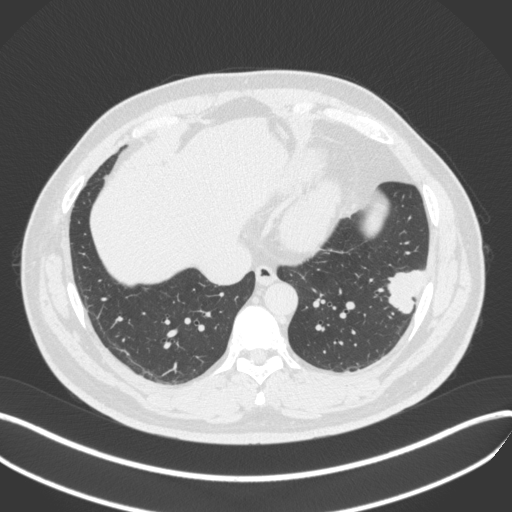
Chest CT, one axial slice. Slice 129 of 420 in the series (ordered by position). Reconstruction kernel B31f. Lung window (W 1500 / L -600 HU). 1 mm slice thickness. 512 × 512 image matrix, field of view 400 × 400 mm. Male patient, age 39 years. Case-level facts recorded for this patient, not image findings: clinical TNM (as recorded): T2a N0 M0.
Structures marked on this image (rectangle marked by the reading radiologist):
- lung tumour (recorded histology: adenocarcinoma): bounding box <381,266,430,316> (left, top, right, bottom; pixels)